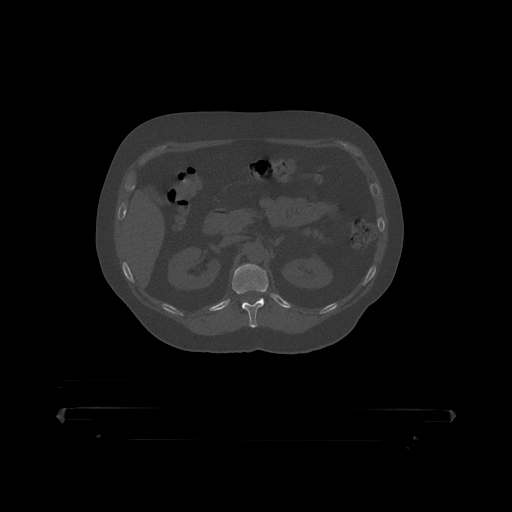
CT including the spine, one axial slice. Position 165 of 390 along the scan axis. Reconstruction kernel STANDARD. 120 kVp. Bone window (W 1800 / L 400 HU). 512 × 512 image matrix. Male patient, age 60 years. From the clinical record (not read from this slice): primary cancer: prostate.
Structures marked on this image (semi-automatic segmentation, software-assisted and operator-edited):
- T12 vertebra: bounding box [x1, y1, x2, y2] px = [232, 264, 269, 319]